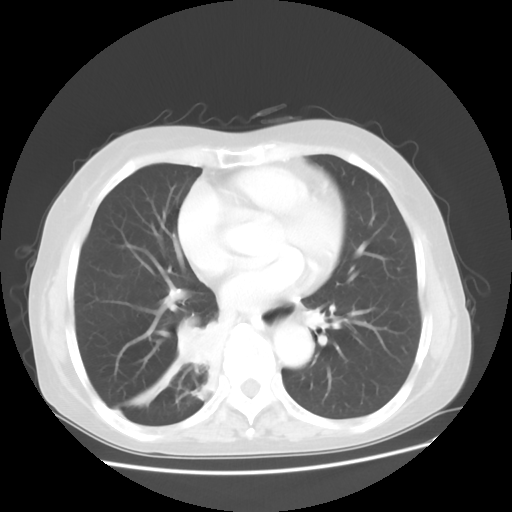
Chest CT, one axial slice. Position 18 of 48 along the scan axis. Lung window (W 1500 / L -600 HU). 5 mm slice thickness. 512 × 512 image matrix, field of view 360 × 360 mm. Patient: female, 63 years. From the clinical record (not read from this slice): clinical TNM (as recorded): T2 N3 M1b; histopathological grade: G3.
Annotated regions visible in this slice (rectangle marked by the reading radiologist):
- lung tumour (recorded histology: small cell carcinoma): bounding box [x1, y1, x2, y2] px = [175, 322, 228, 377]